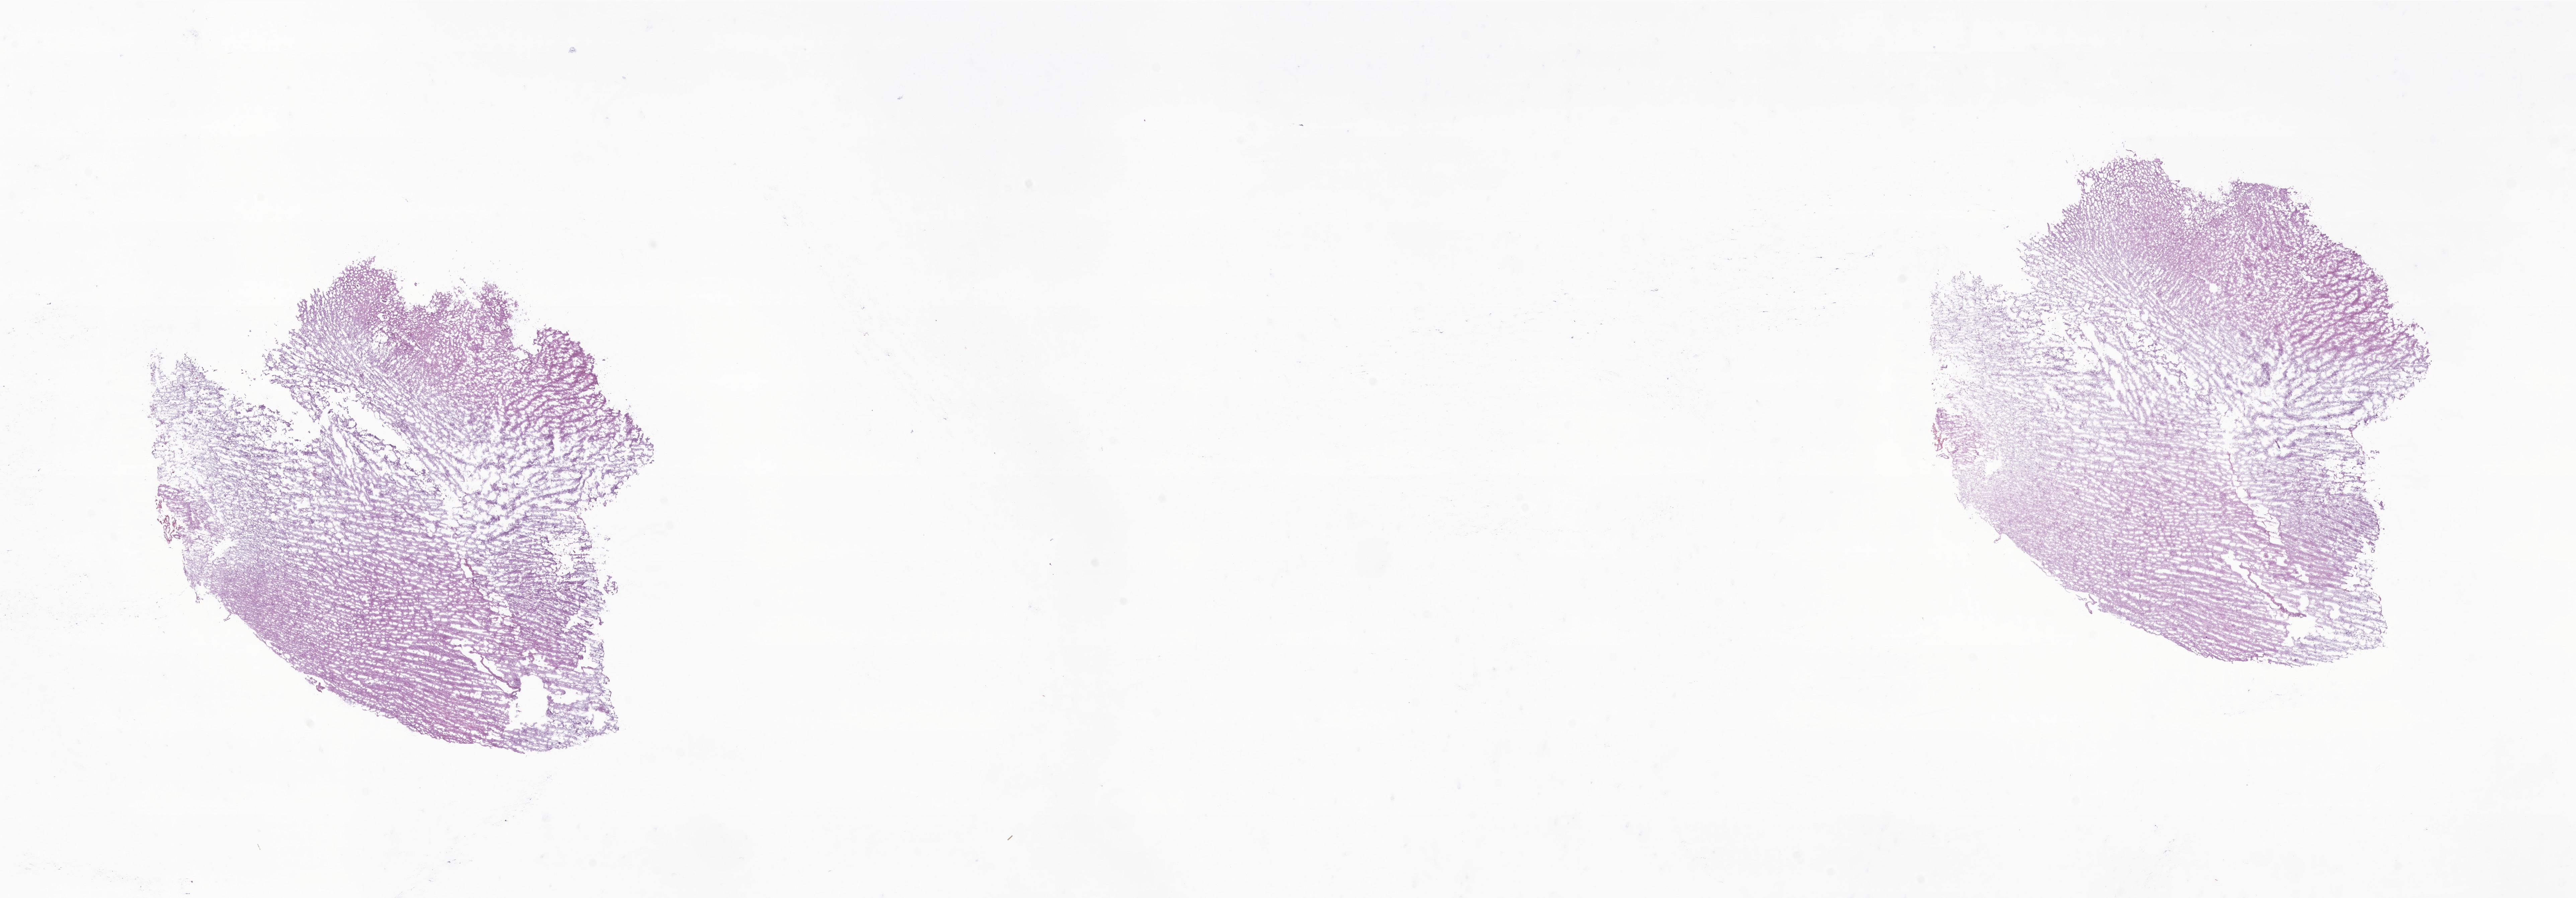
Whole-slide image, haematoxylin and eosin stain of tumor tissue from the parietal lobe — whole scanned area (about 32.4 x 11.3 mm) shown as a low-resolution overview, frozen section (OCT-embedded). Male patient, age 84 months (7 years).
* diagnosis: Astrocytoma, NOS